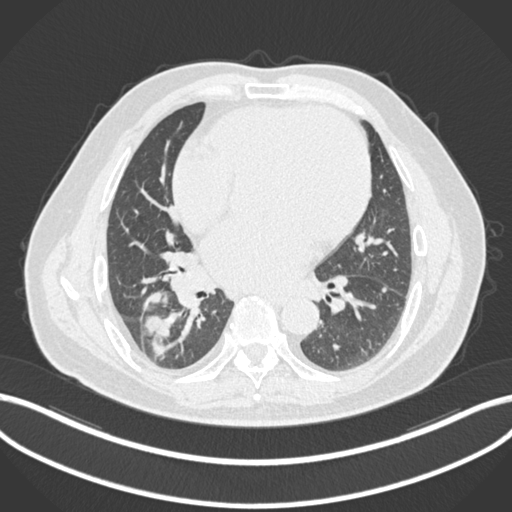
Chest CT, one axial slice. Slice 80 of 200 in the series (ordered by position). Reconstruction kernel B30f. 120 kVp. Lung window (W 1500 / L -600 HU). 512 × 512 image matrix. Patient: male, 59 years.
Structures marked on this image (rectangle marked by the reading radiologist):
- lung tumour (recorded histology: adenocarcinoma): bounding box <139,289,173,360> (left, top, right, bottom; pixels)